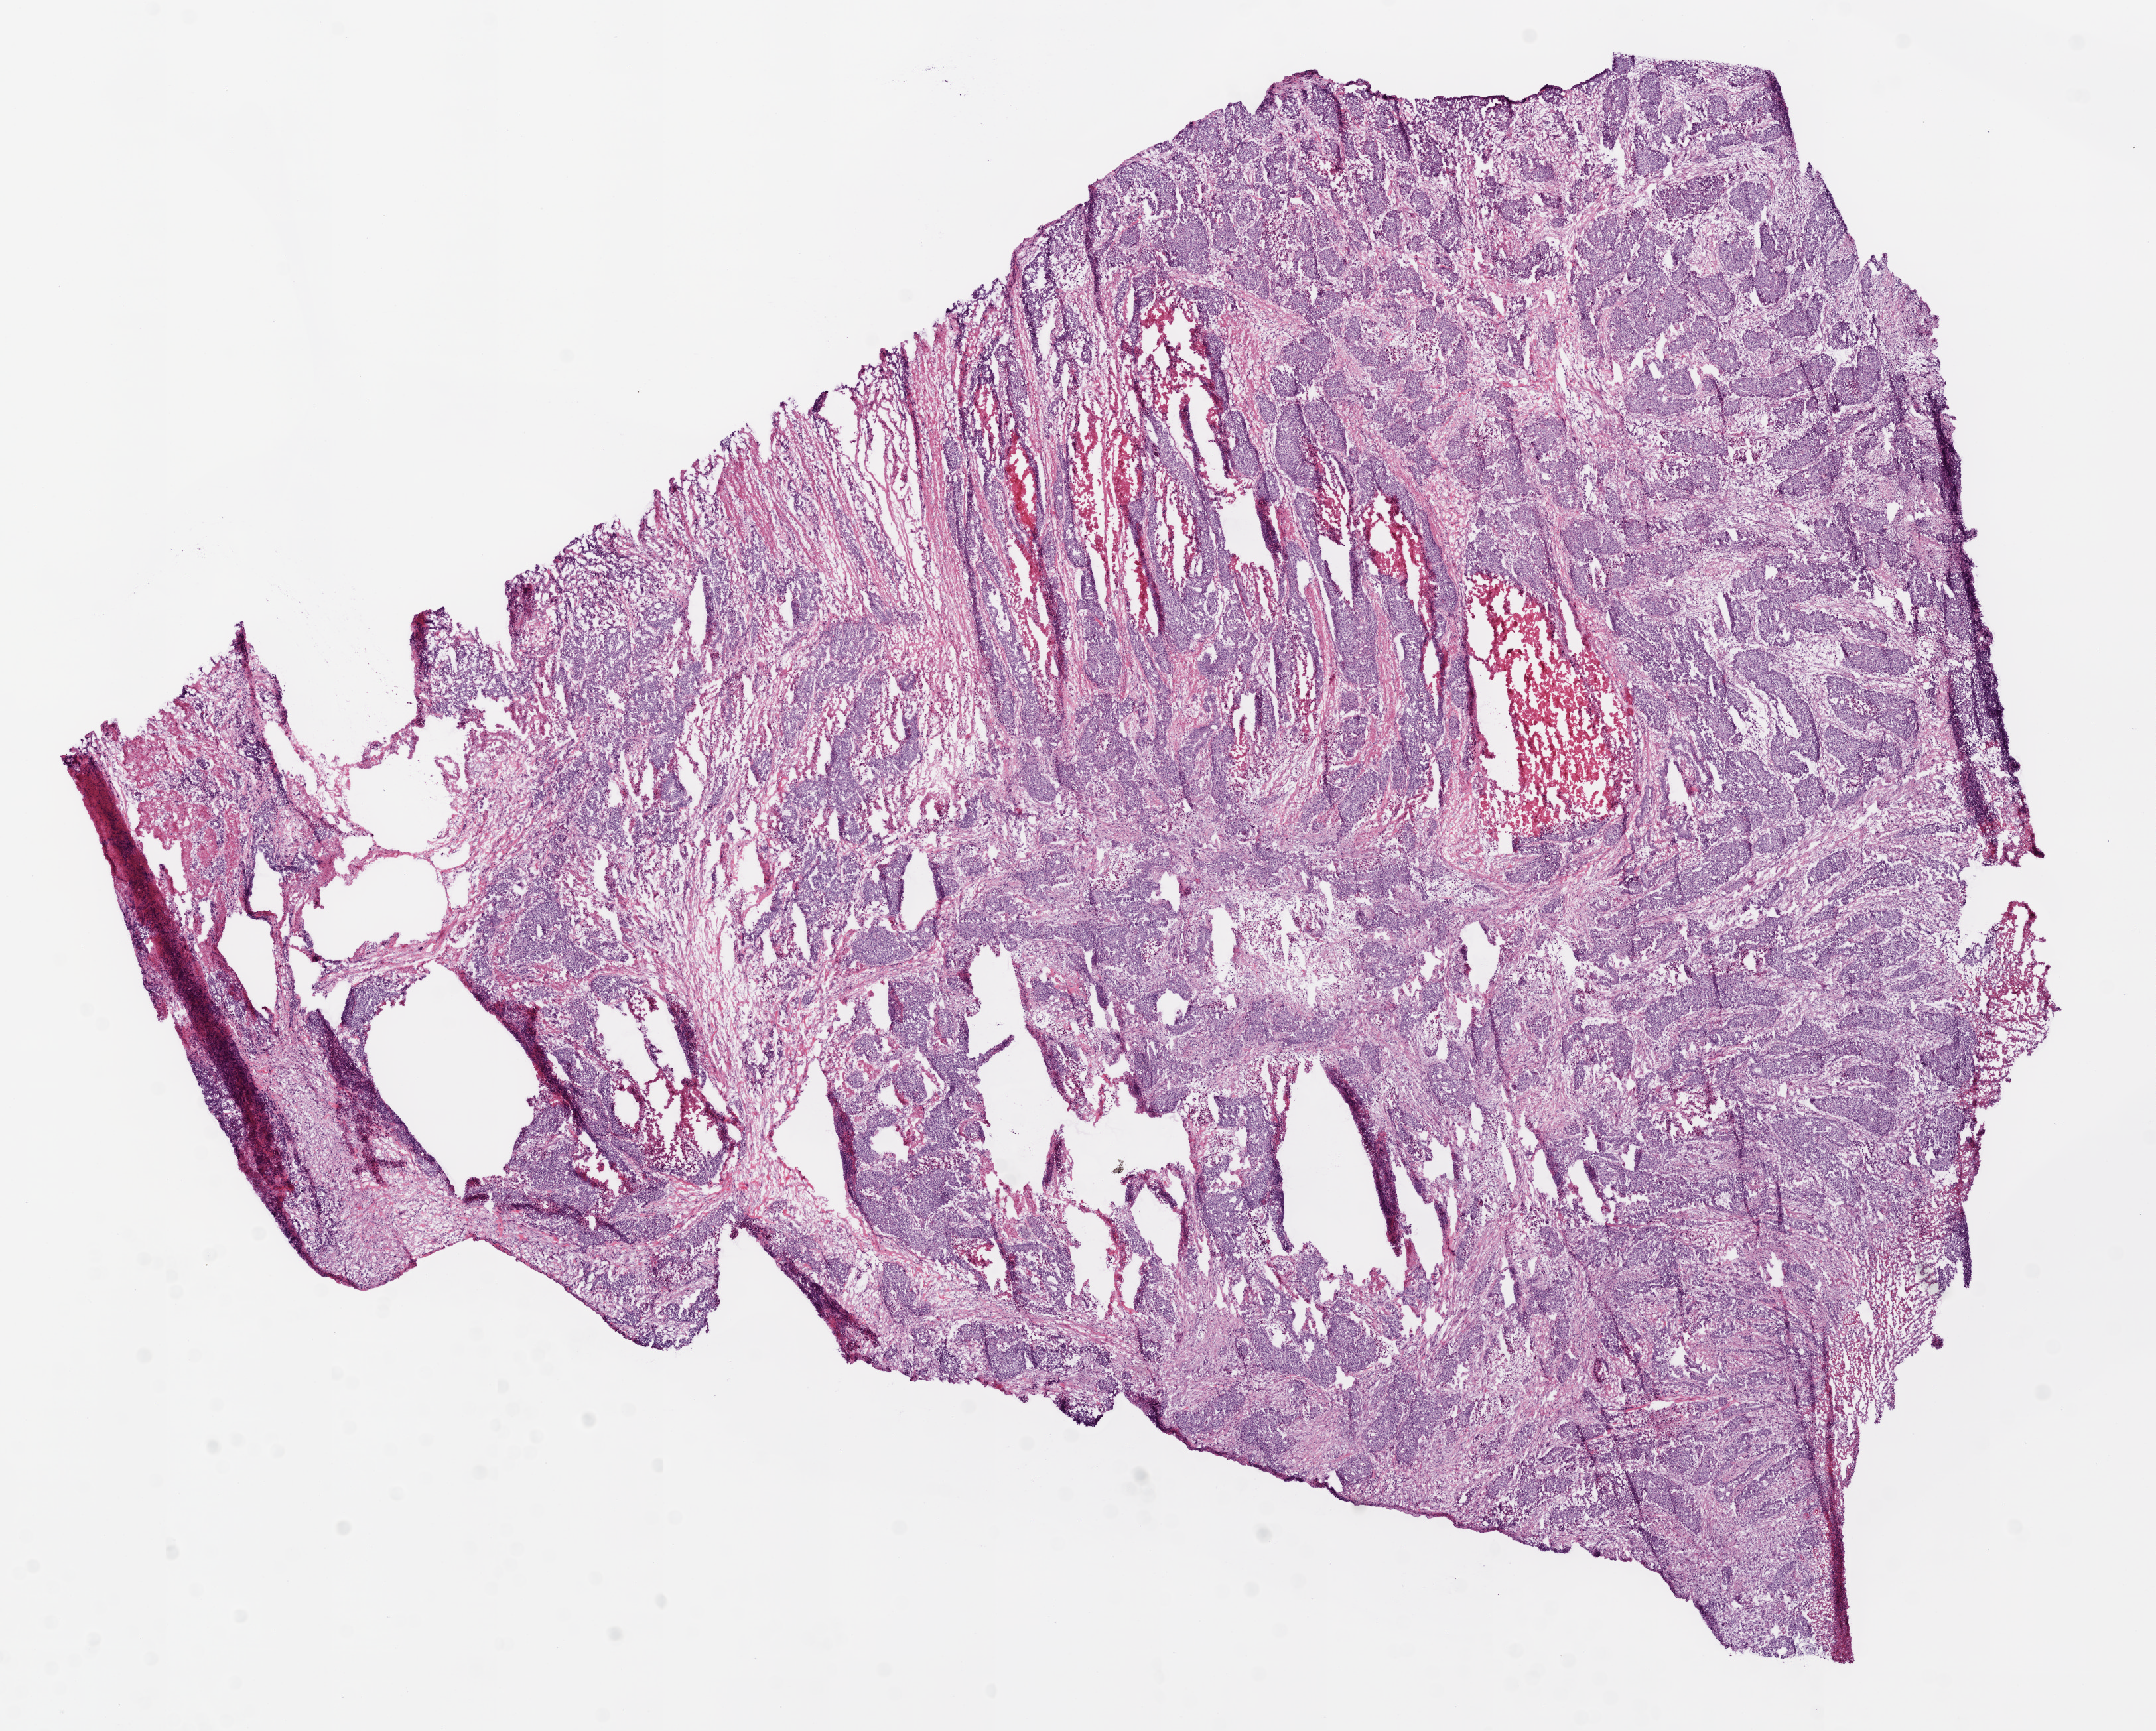
H&E-stained whole-slide image — shown as a low-resolution overview of the whole scanned area (about 13.0 x 10.5 mm, from a 20x scan), frozen section from the bottom of the tissue portion, sample: primary tumour, rectum. Female, age 84 years at initial diagnosis. Composition of this section per pathologist review: tumour cells 75%, tumour nuclei 80%, normal cells 0%, stromal cells 15%, necrosis 10%.
Histologic diagnosis: Adenocarcinoma, NOS. AJCC pathologic stage: IV (5th edition).